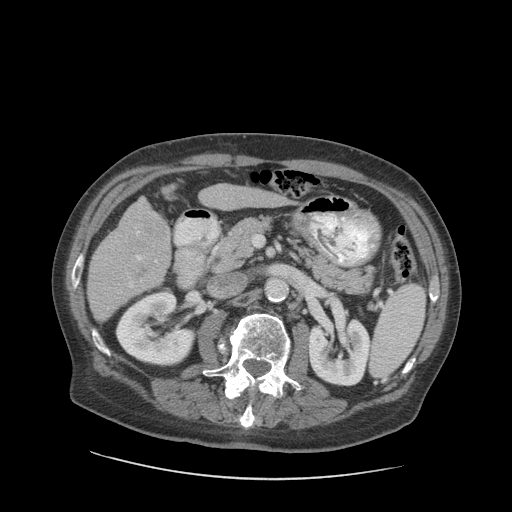
Contrast-enhanced abdominal CT (liver protocol), one axial slice; slice 38 of 89 in the series (ordered by position); reconstruction kernel STANDARD; 140 kVp; soft-tissue window (W 400 / L 40 HU); 2.5 mm slice thickness; 512 × 512 image matrix, field of view 420 × 420 mm. From the clinical record (not read from this slice): diagnosis: hepatocellular carcinoma (patient treated with transarterial chemoembolisation; whether this scan precedes or follows treatment is not stated here); TNM stage (as recorded): Stage-I; Child-Pugh class: A; tumour differentiation: moderately differentiated; tumour nodularity: uninodular.
Outlined on this slice (semi-automatic segmentation, software-assisted and operator-edited):
- liver parenchyma outside the tumour (the mass and vessels are separate outlines, so this box may not span the whole liver): bounding box <88,192,278,321> (left, top, right, bottom; pixels)
- mass: <126,209,169,281>
- liver vessels: <129,256,158,287>